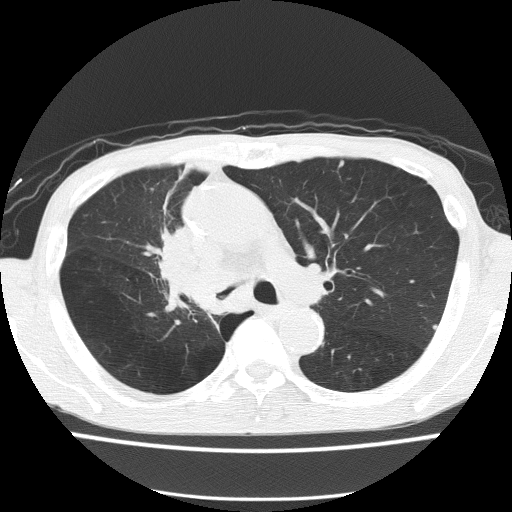
Low-dose screening chest CT, one axial slice. Position 97 of 150 along the scan axis. 120 kVp. Lung window (W 1500 / L -600 HU). 2 mm slice thickness. 512 × 512 image matrix, field of view 336 × 336 mm.
Outlined on this slice (expert manual segmentation):
- lesion 1 (tumor, hilum of right lung): bounding box [x1, y1, x2, y2] px = [162, 229, 219, 311]